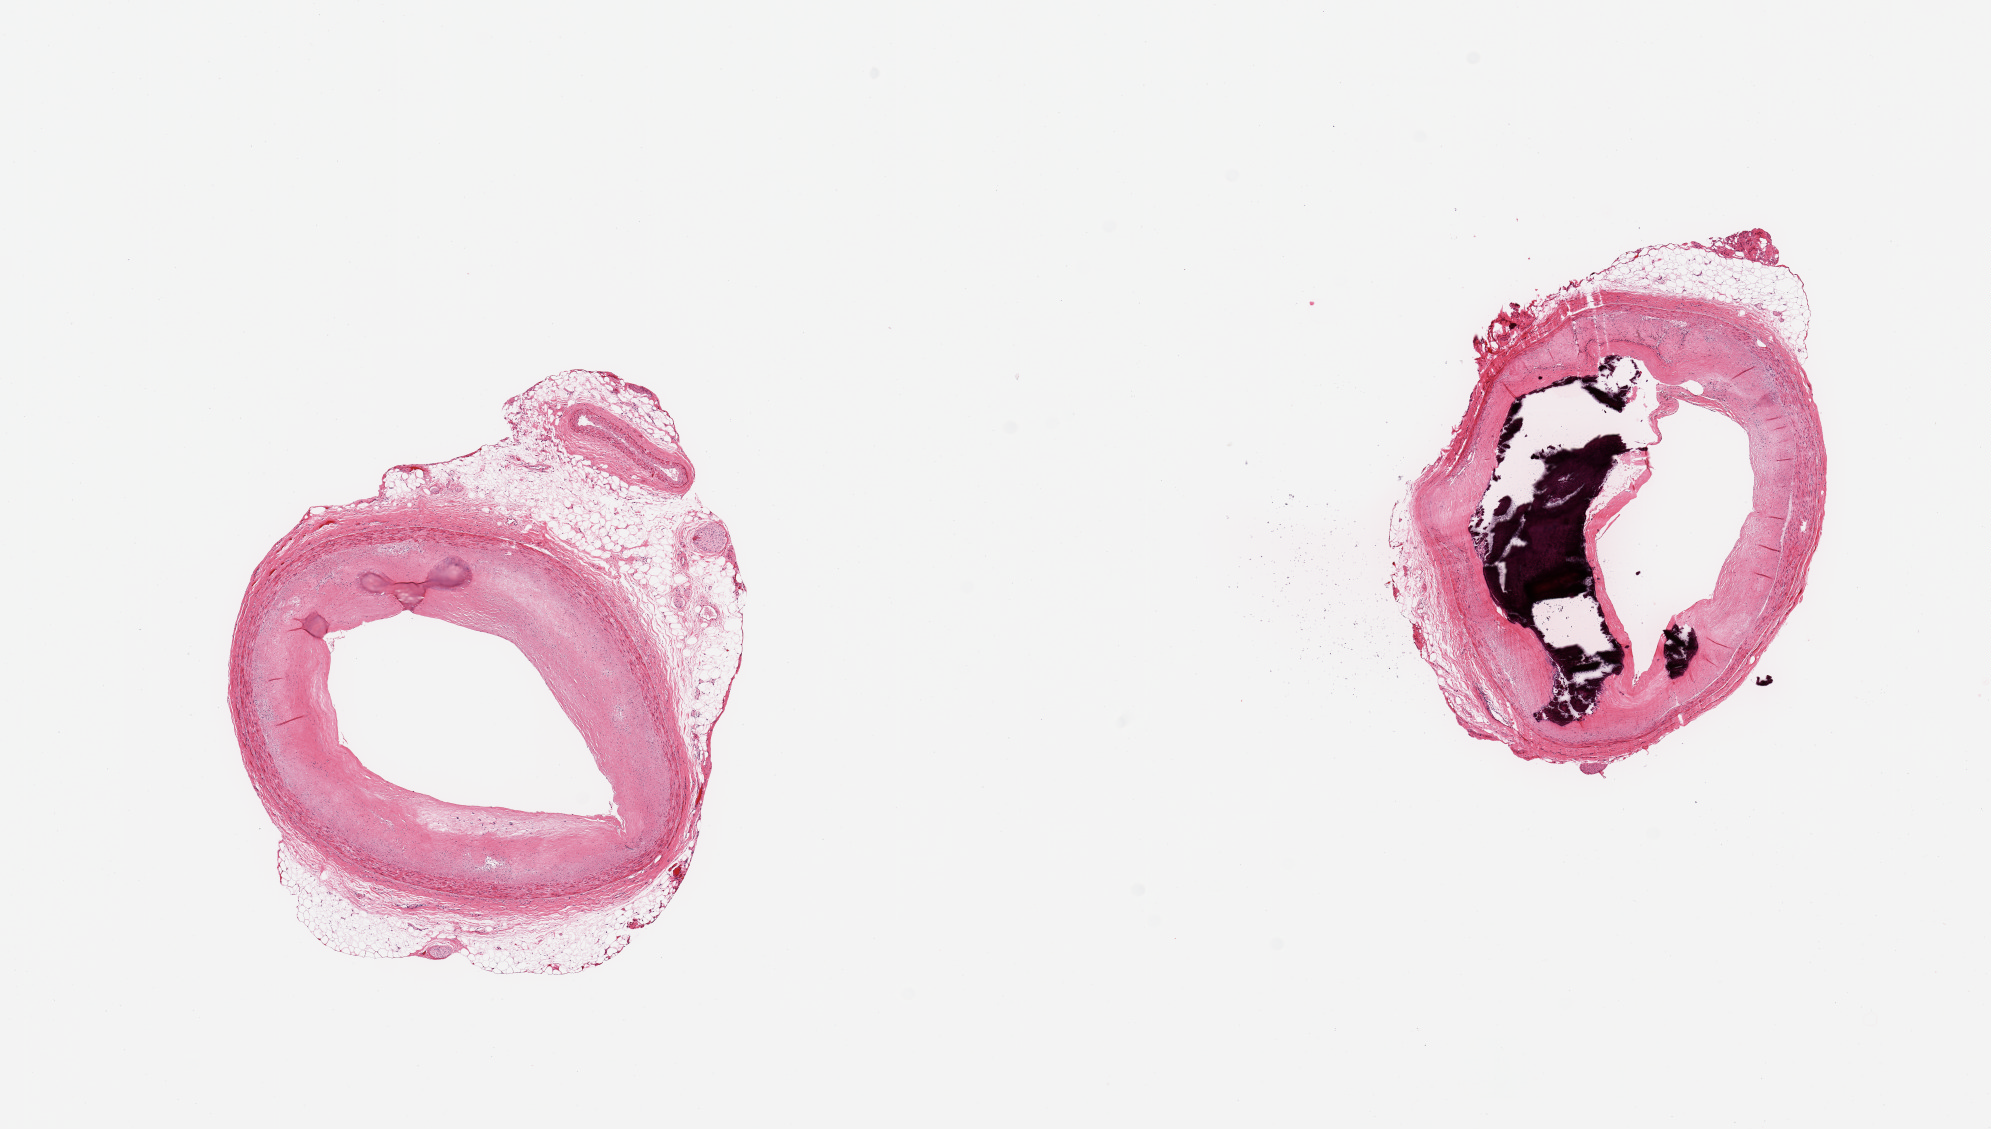
Digitized H&E-stained section — low-resolution overview of the scanned area, about 15.8 x 8.9 mm. PAXgene-fixed, paraffin-embedded tissue. Sampled site (target tissue): coronary artery. Donor tissue sample.
Reviewer comment on this tissue sample: 2 pieces; calcific atherosclerosis with luminal narrowing of 50-75%, partial rim of attached fat up to 10-30%.